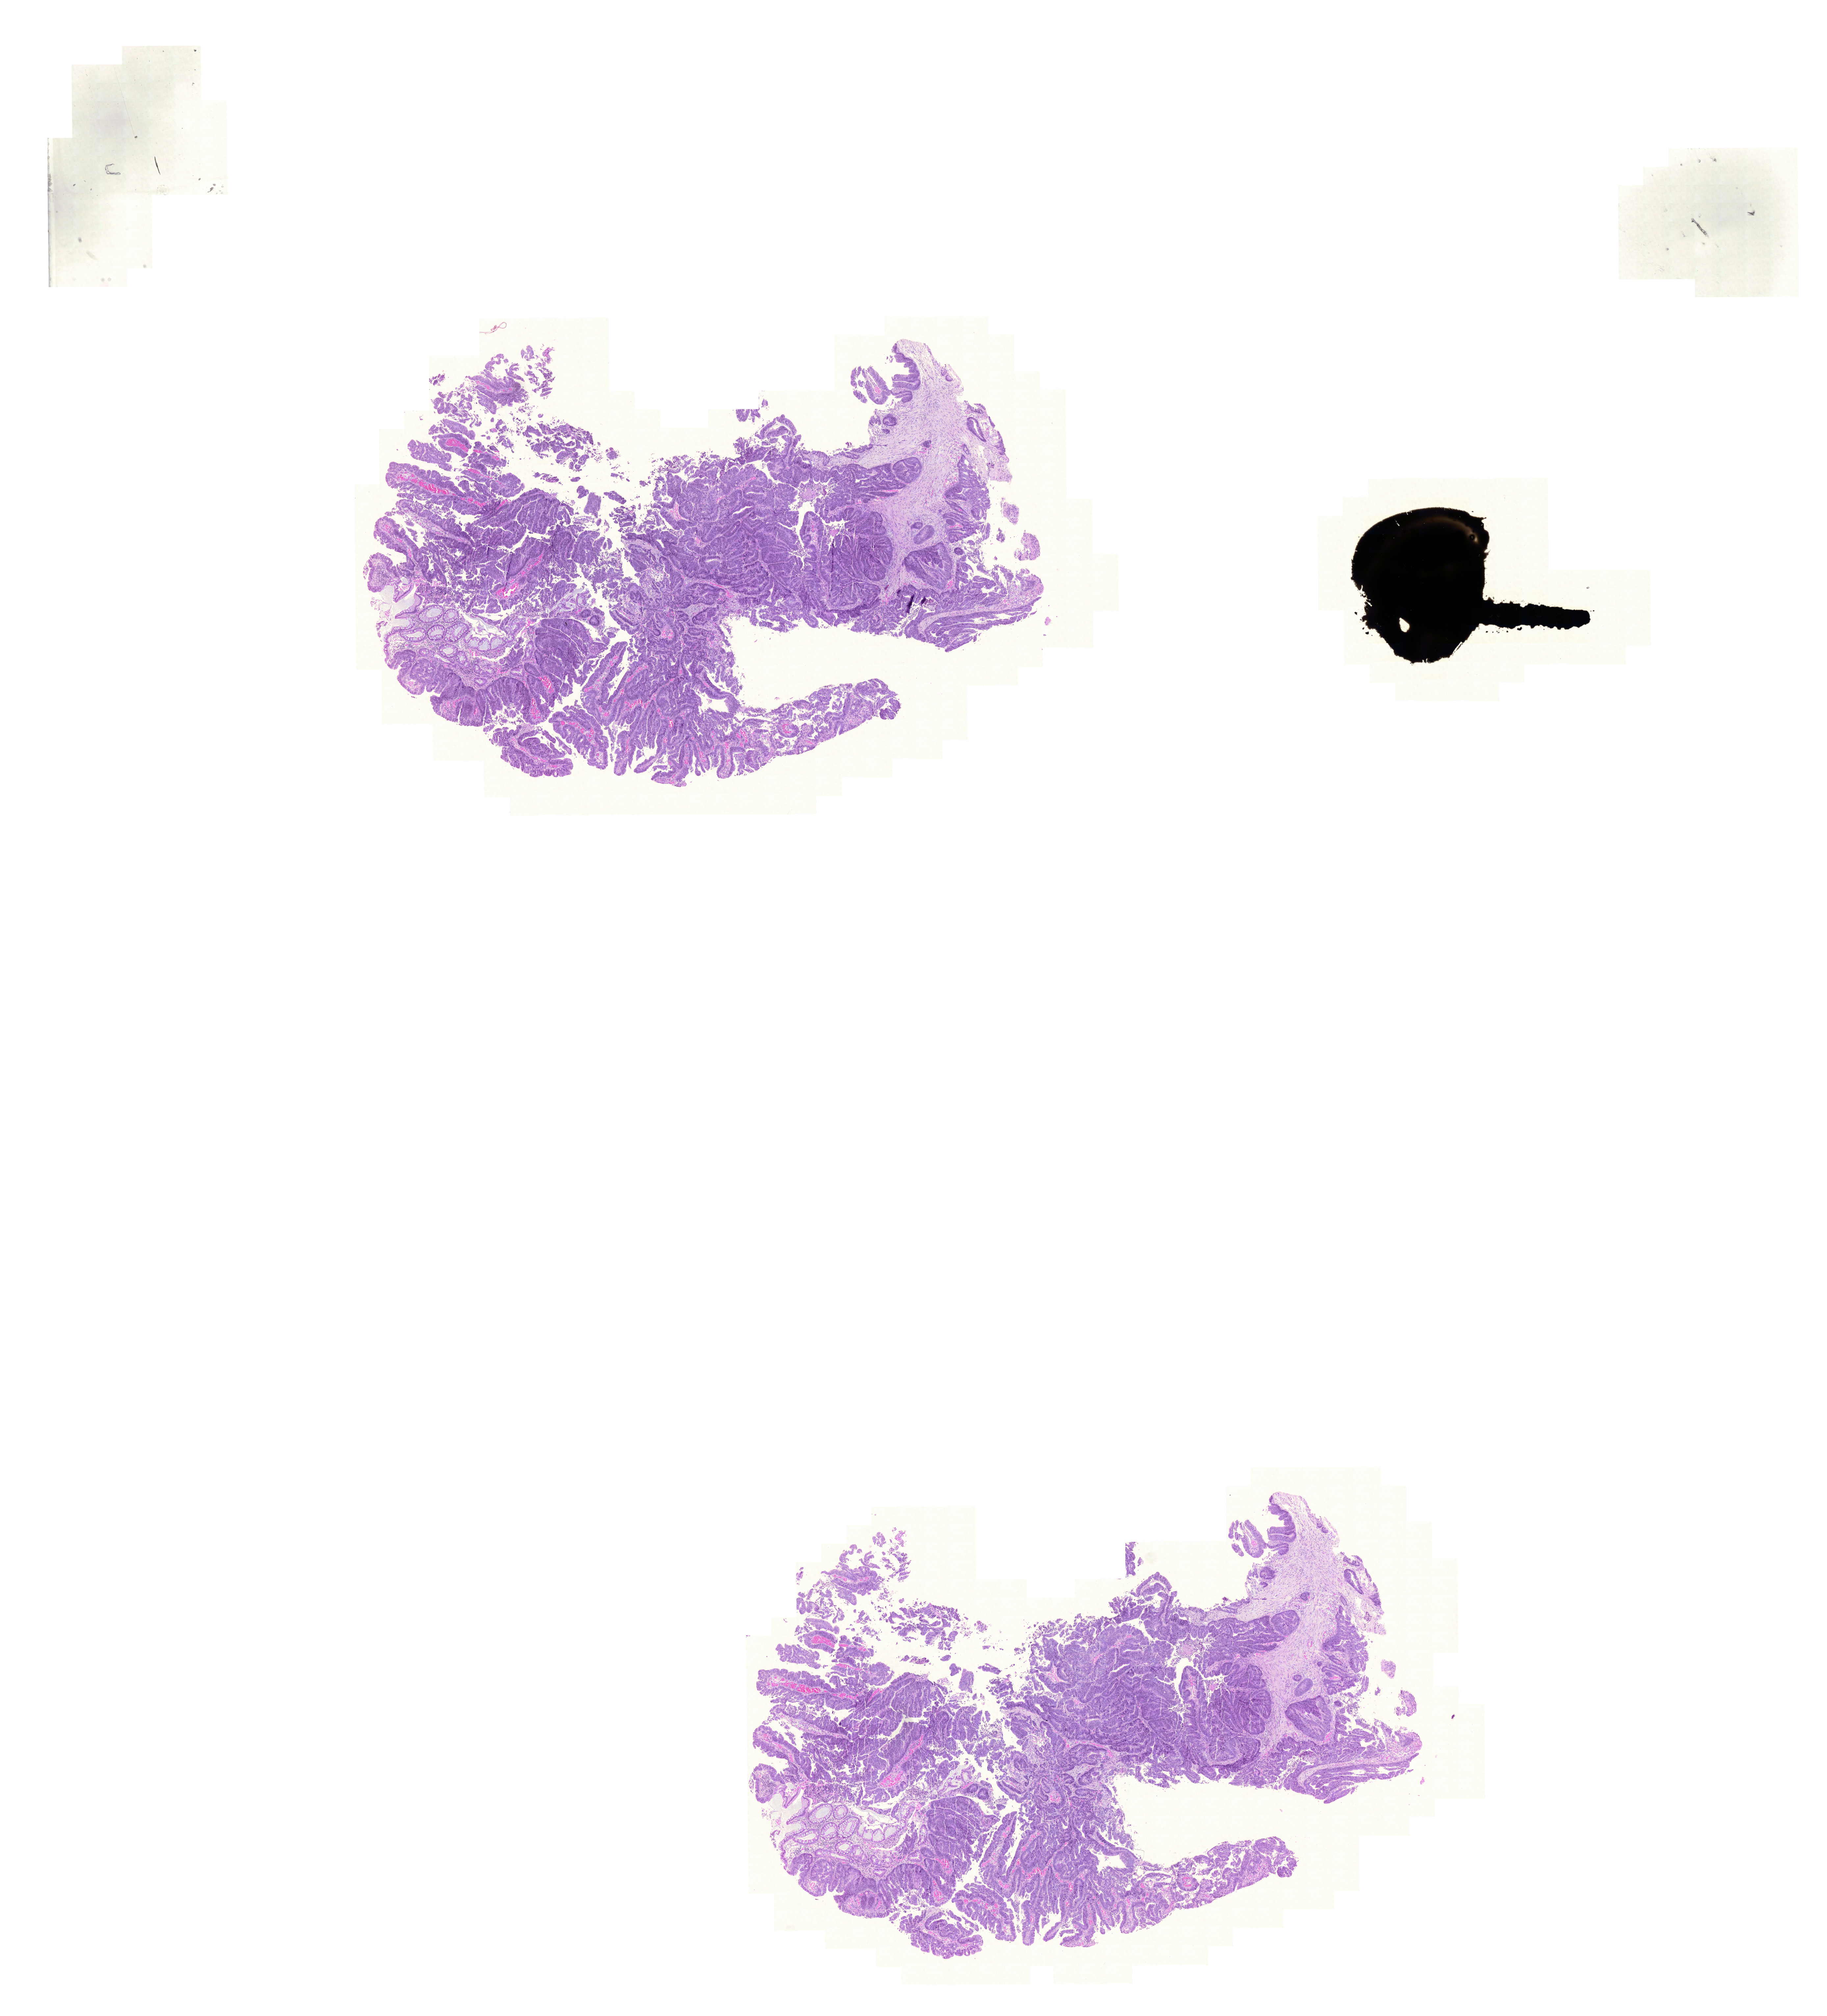
Whole-slide histology image, H&E — whole scanned area (about 20.7 x 22.8 mm, from a 20x scan) shown as a low-resolution overview, formalin-fixed paraffin-embedded (FFPE) diagnostic section, primary tumour sample from the colon. Female, age 70 years at initial diagnosis.
Diagnosis: Adenocarcinoma, NOS.